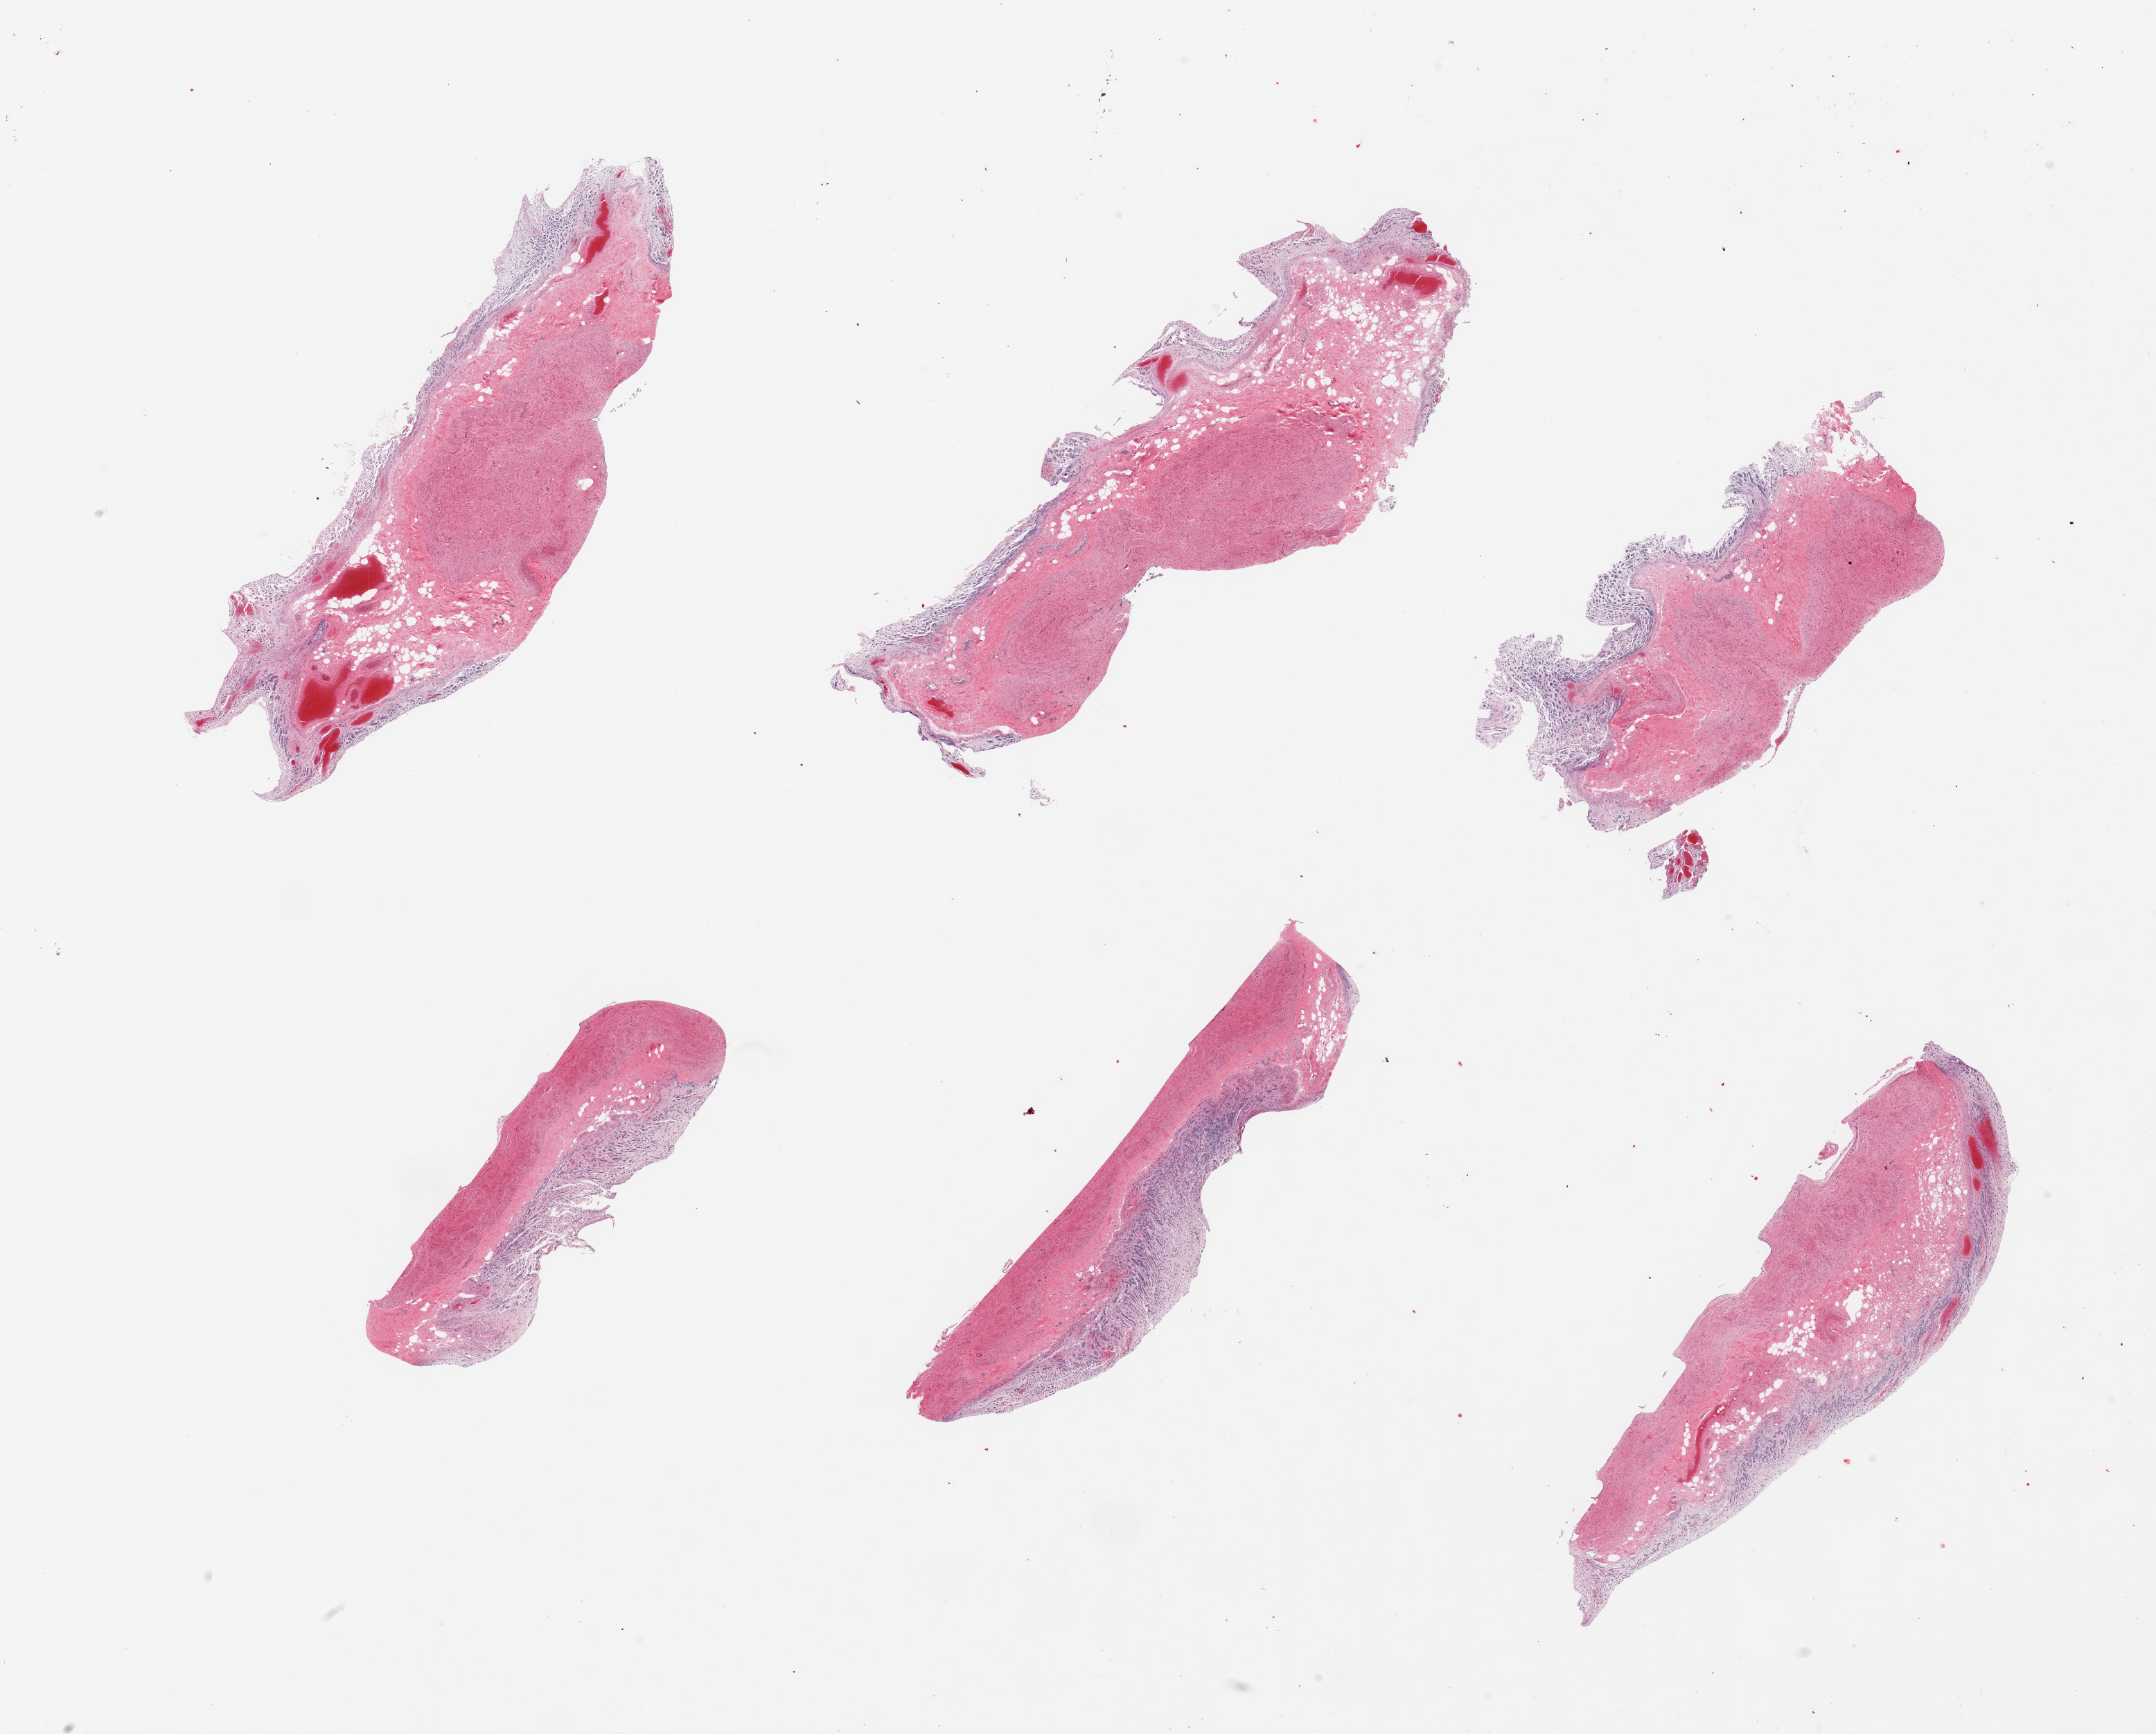
Whole-slide image, haematoxylin and eosin stain — a low-resolution overview of the entire scanned area, about 24.6 x 19.8 mm; PAXgene-fixed paraffin-embedded (PFPE) section; target tissue: stomach; tissue donor sample. Donor: male.
Review note (as recorded): 6 pieces; full thickness sections, mucosa (3), muscularis (2).